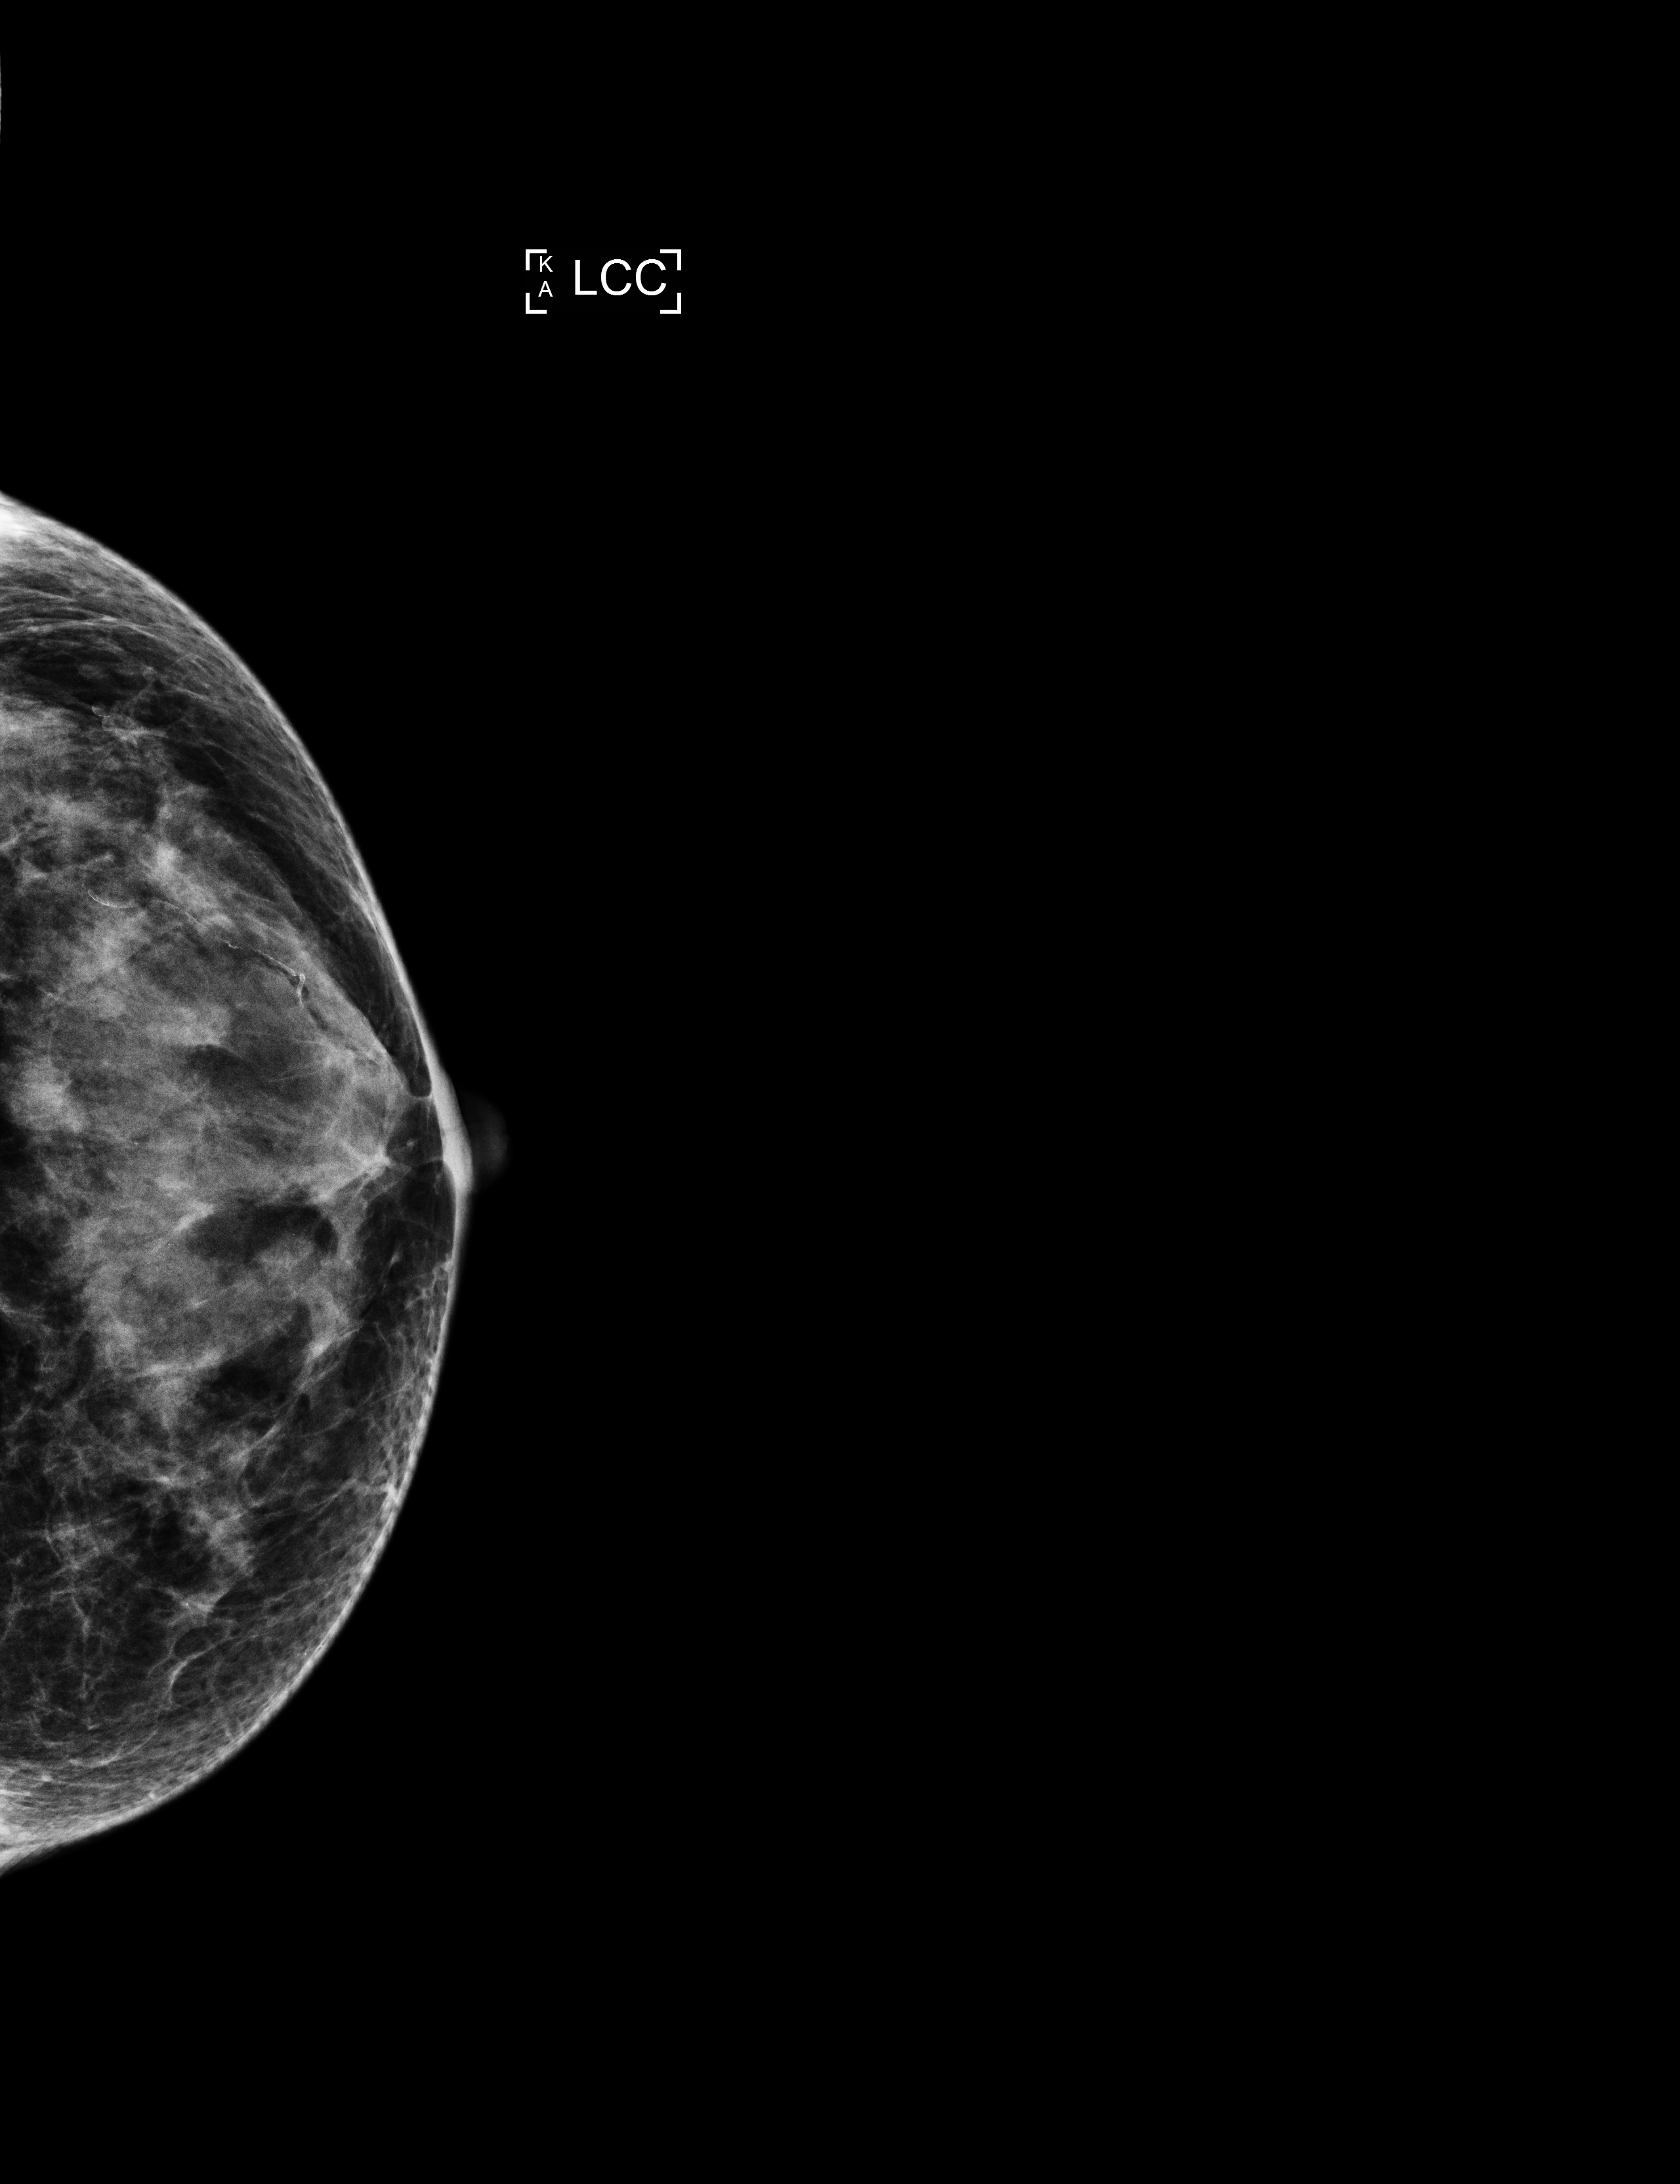
Screening examination, compressed breast thickness 39 mm, system: Selenia Dimensions. Patient: female, 59 years.
Image type: full-field digital mammogram. Breast: left. Projection: cranio-caudal projection.